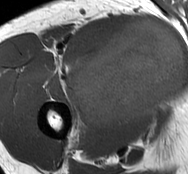
MRI of an extremity soft-tissue mass, one axial slice; slice 51 of 93 in the series (ordered by position); MR volume resampled by the dataset authors to the PET/CT grid (not the native acquisition matrix); 3.27 mm slice thickness; 188 × 174 image matrix, field of view 184 × 170 mm. Male patient. From the clinical record (not read from this slice): histological type: undifferentiated - pleiomorphic; grade: high; site of the primary tumour: right thigh.
Outlined on this slice (expert contour drawn on MRI and transferred to this co-registered scan by the dataset authors):
- gross tumour volume including surrounding oedema: bounding box [x1, y1, x2, y2] px = [72, 19, 185, 130]
- gross tumour volume (mass): [75, 19, 185, 129]